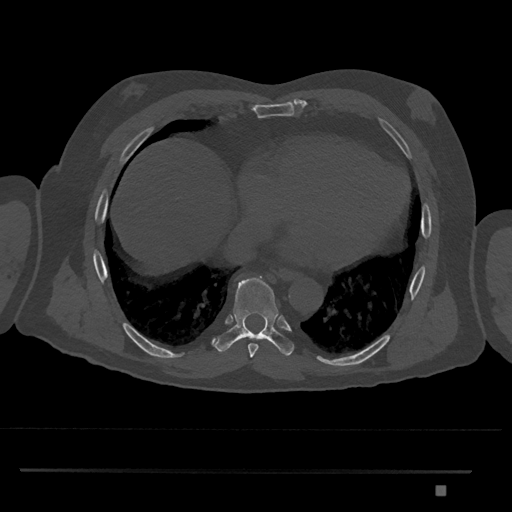
CT including the spine, one axial slice. Slice 1124 of 1134 in the series (ordered by position). 120 kVp. Bone window (W 1800 / L 400 HU). 0.5 mm slice thickness. 512 × 512 image matrix. Patient: male, 65 years. From the clinical record (not read from this slice): primary cancer: prostate.
Outlined on this slice (semi-automatically segmented with operator editing):
- T8 vertebra: bounding box [x1, y1, x2, y2] px = [214, 276, 295, 357]